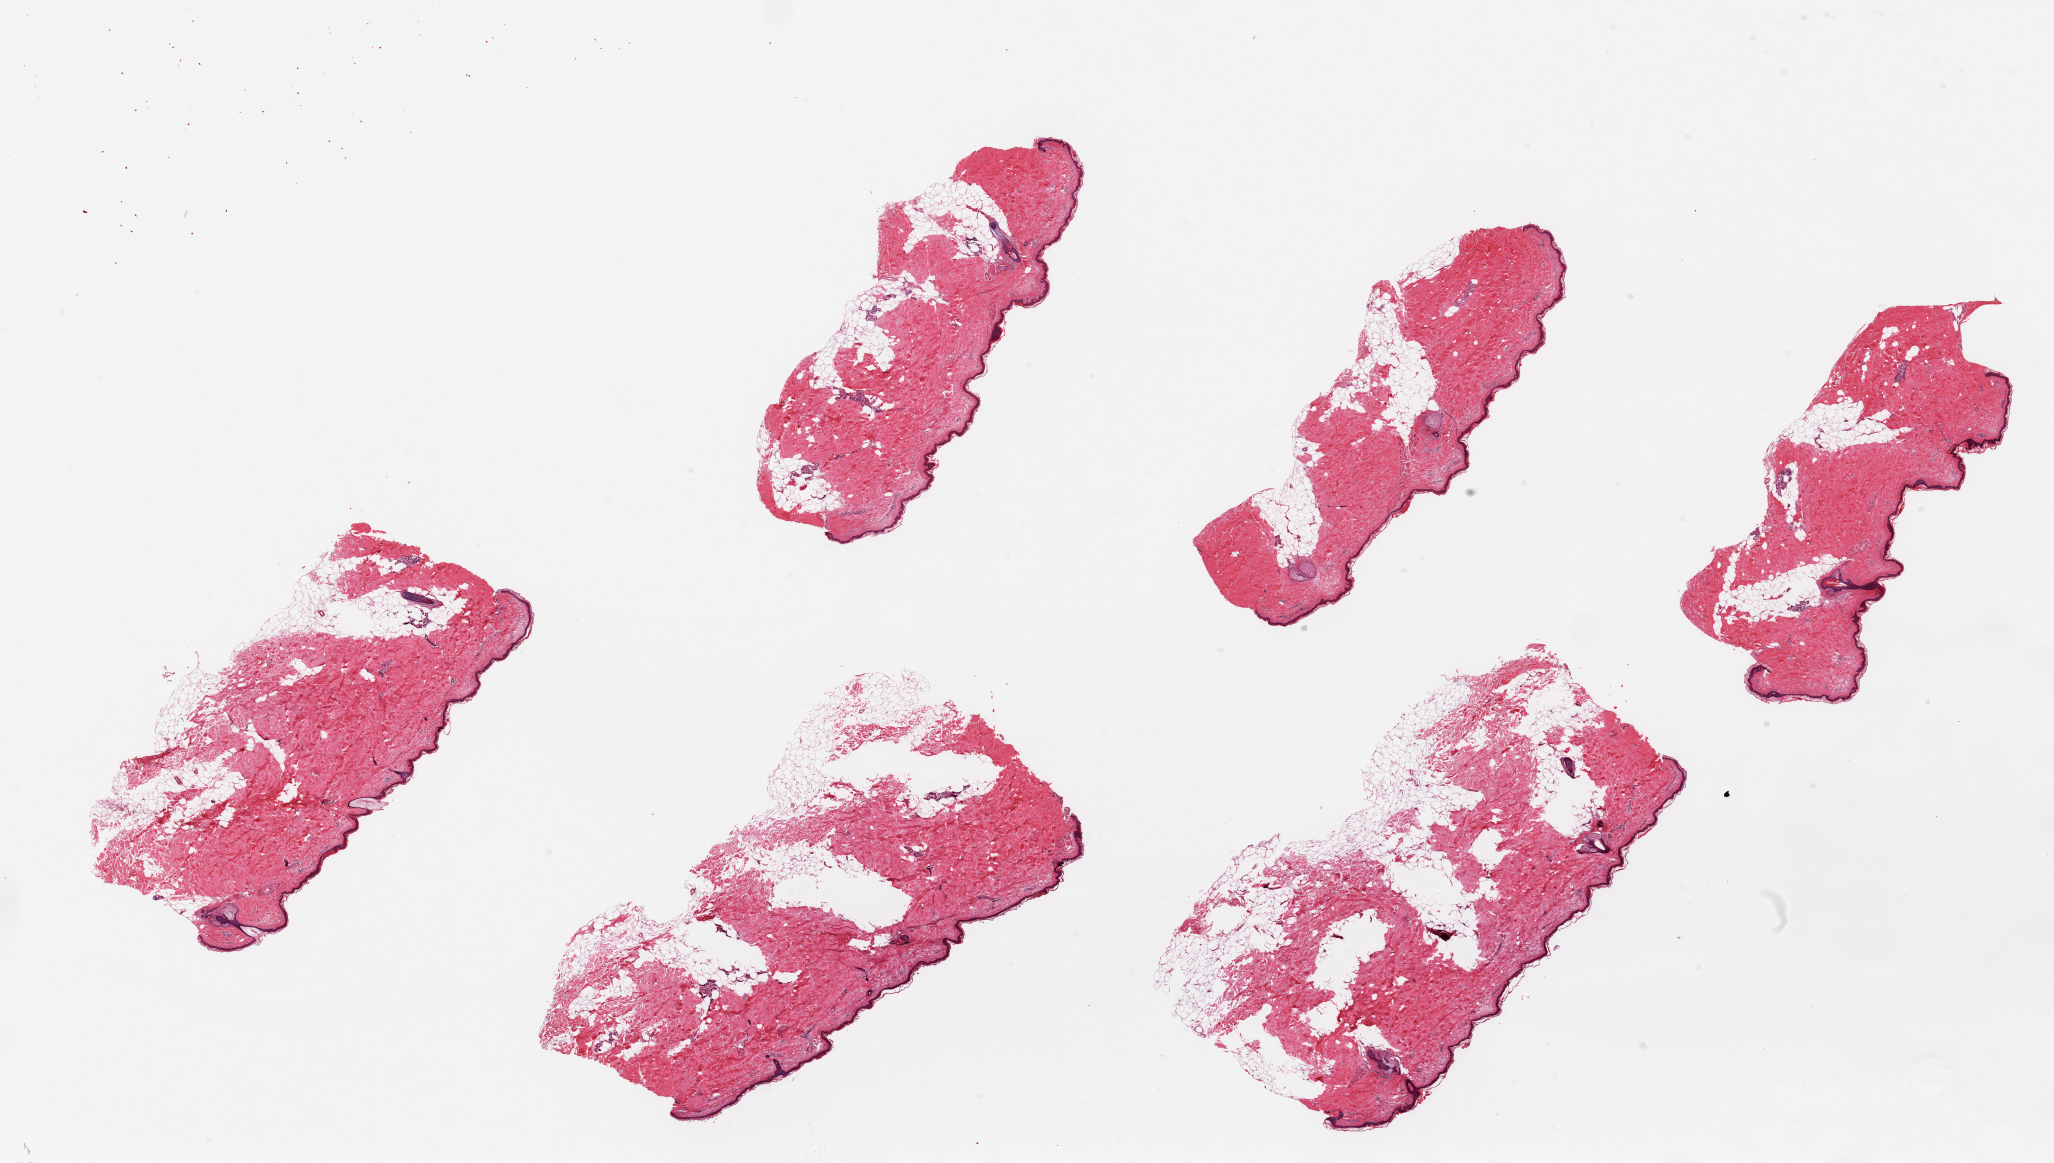
Digitized hematoxylin and eosin (H&E)-stained section, brightfield — low-resolution overview of the scanned area, about 32.5 x 18.4 mm (from a 20x scan), PAXgene-fixed paraffin-embedded (PFPE) section, section of skin of lower leg (target tissue), donor tissue sample. Male donor.
- pathologist's review note for this sample: 6 pieces ~7x3mm. Squamous epithelium is 1-2% of thickness